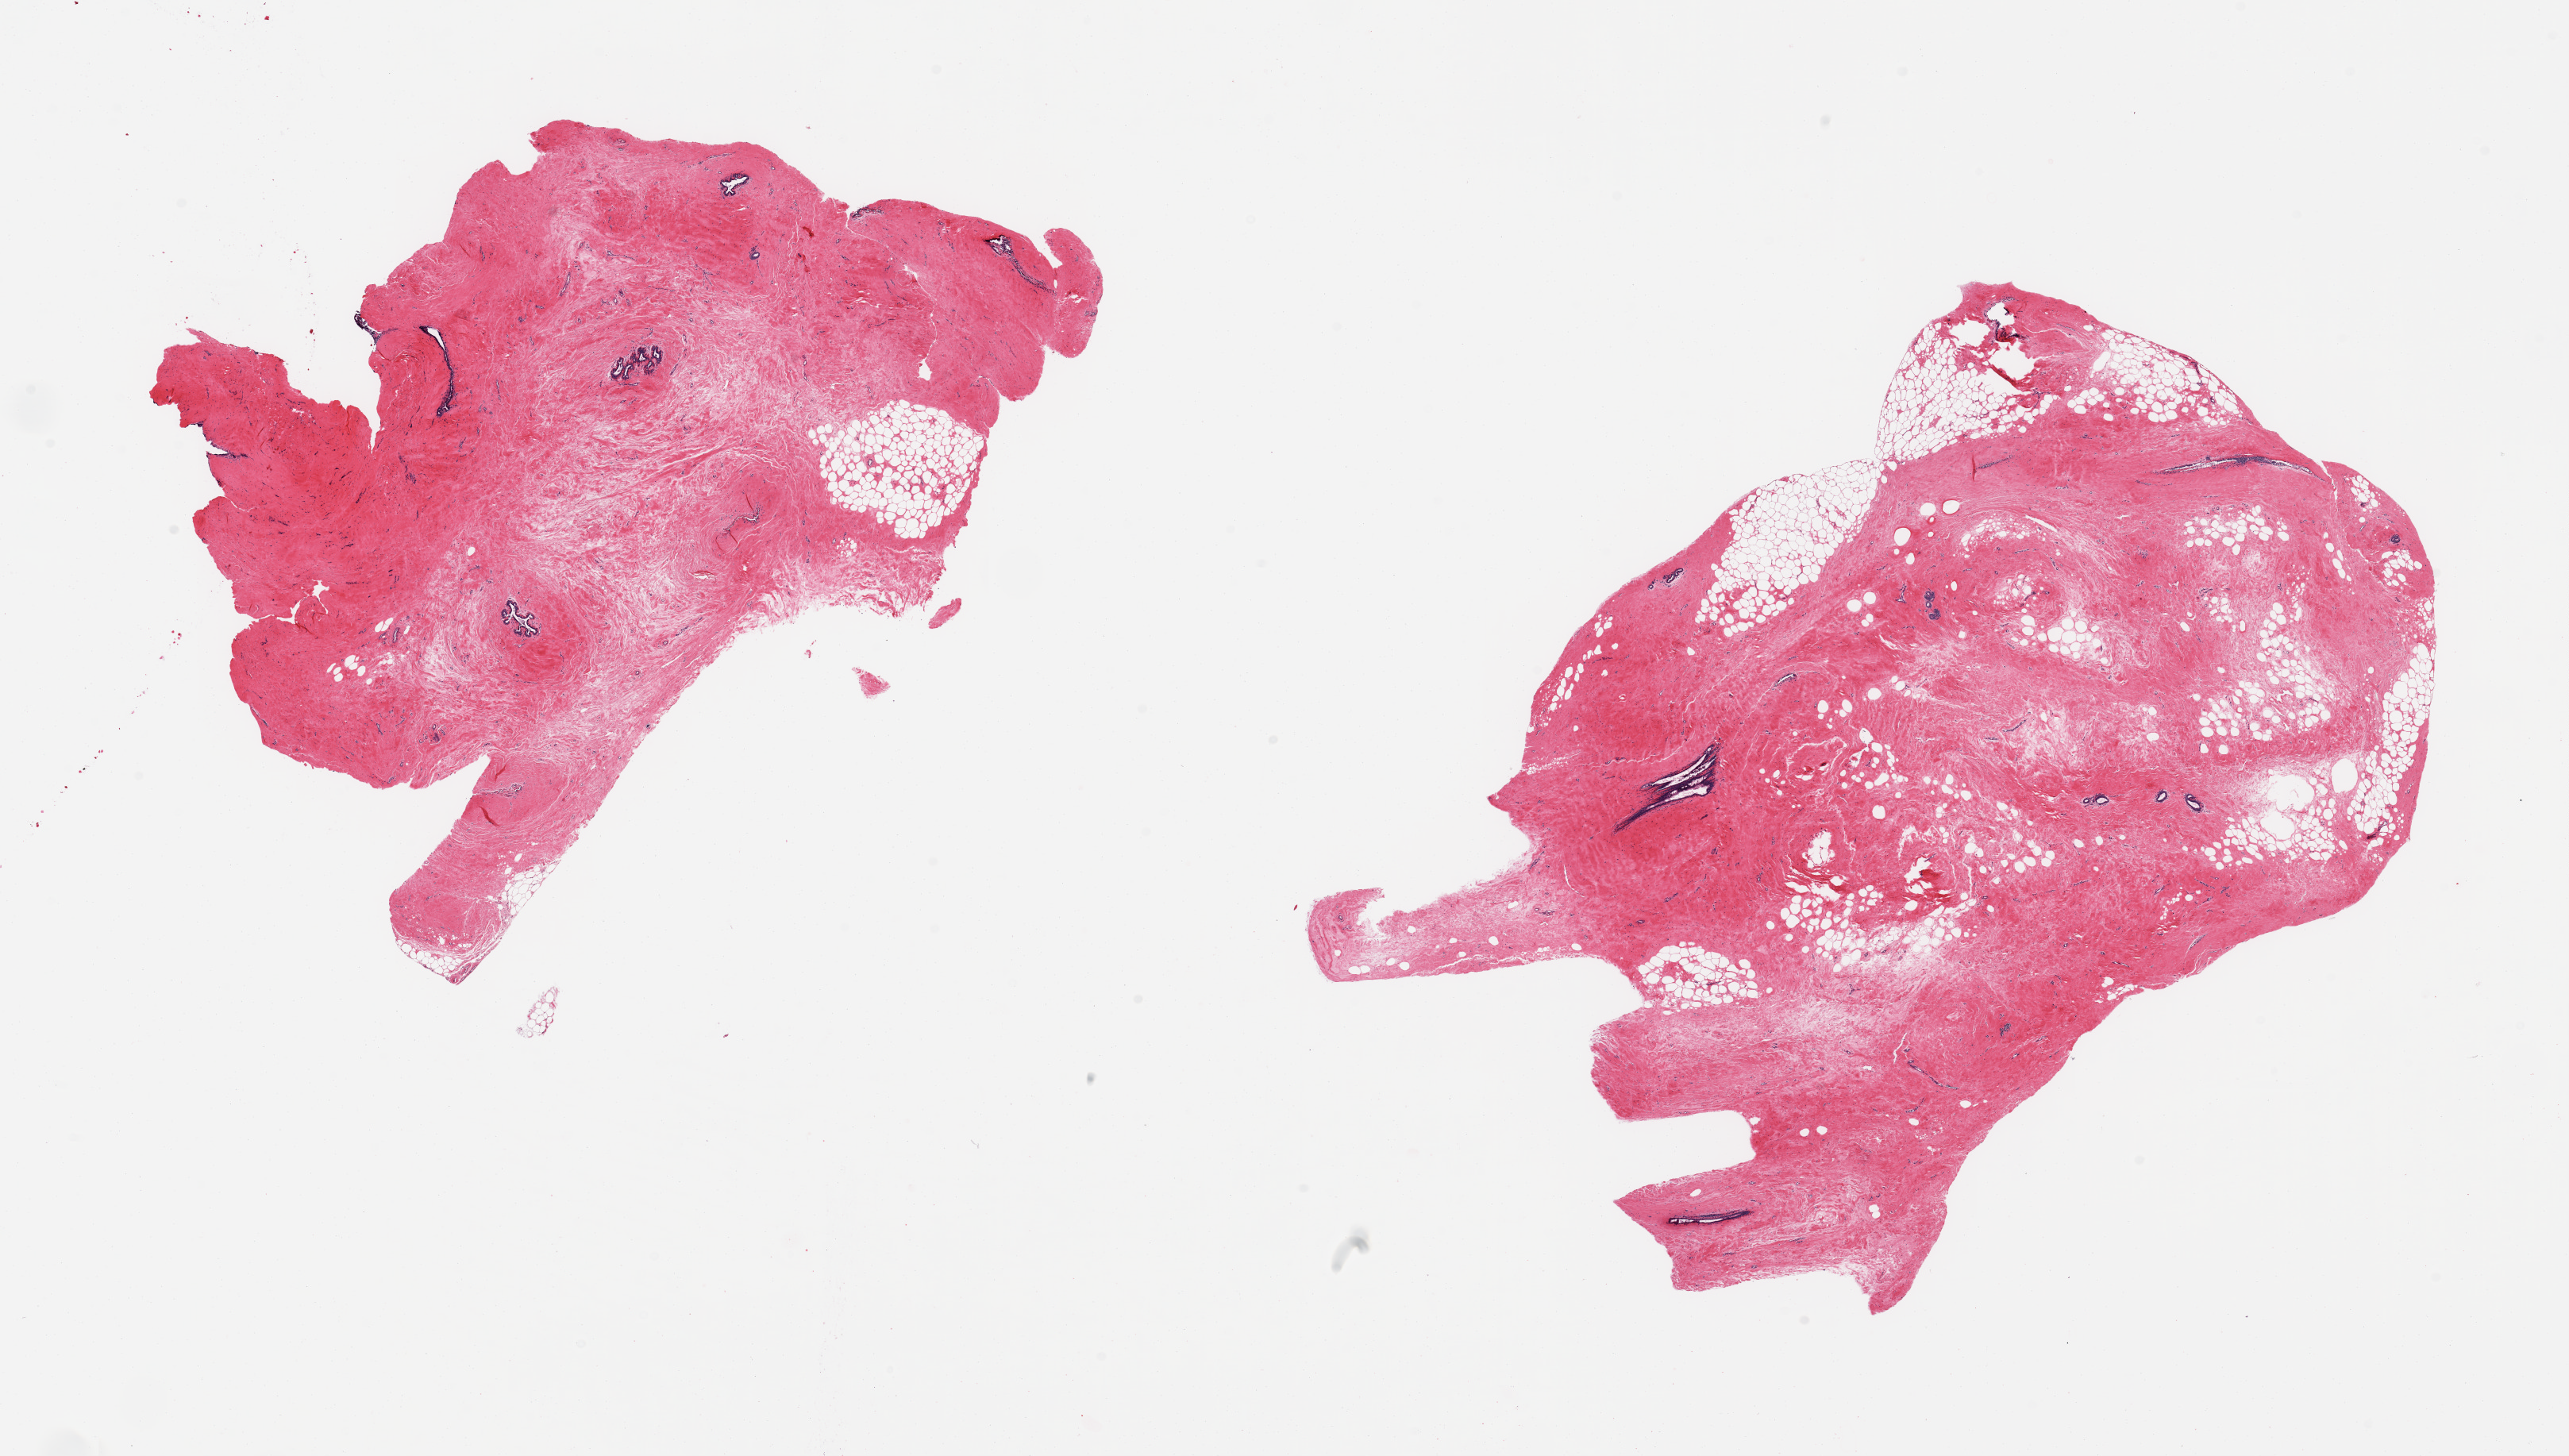
Haematoxylin and eosin whole-slide image, brightfield, shown as a low-resolution overview of the whole scanned area (about 25.6 x 14.5 mm); PAXgene-fixed, paraffin-embedded tissue; sampled site (target tissue): breast; tissue donor sample. Donor sex: male.
Reviewer comment on this tissue sample: 2 pieces, gynecomastoid stromal and ductal hyperplasia.